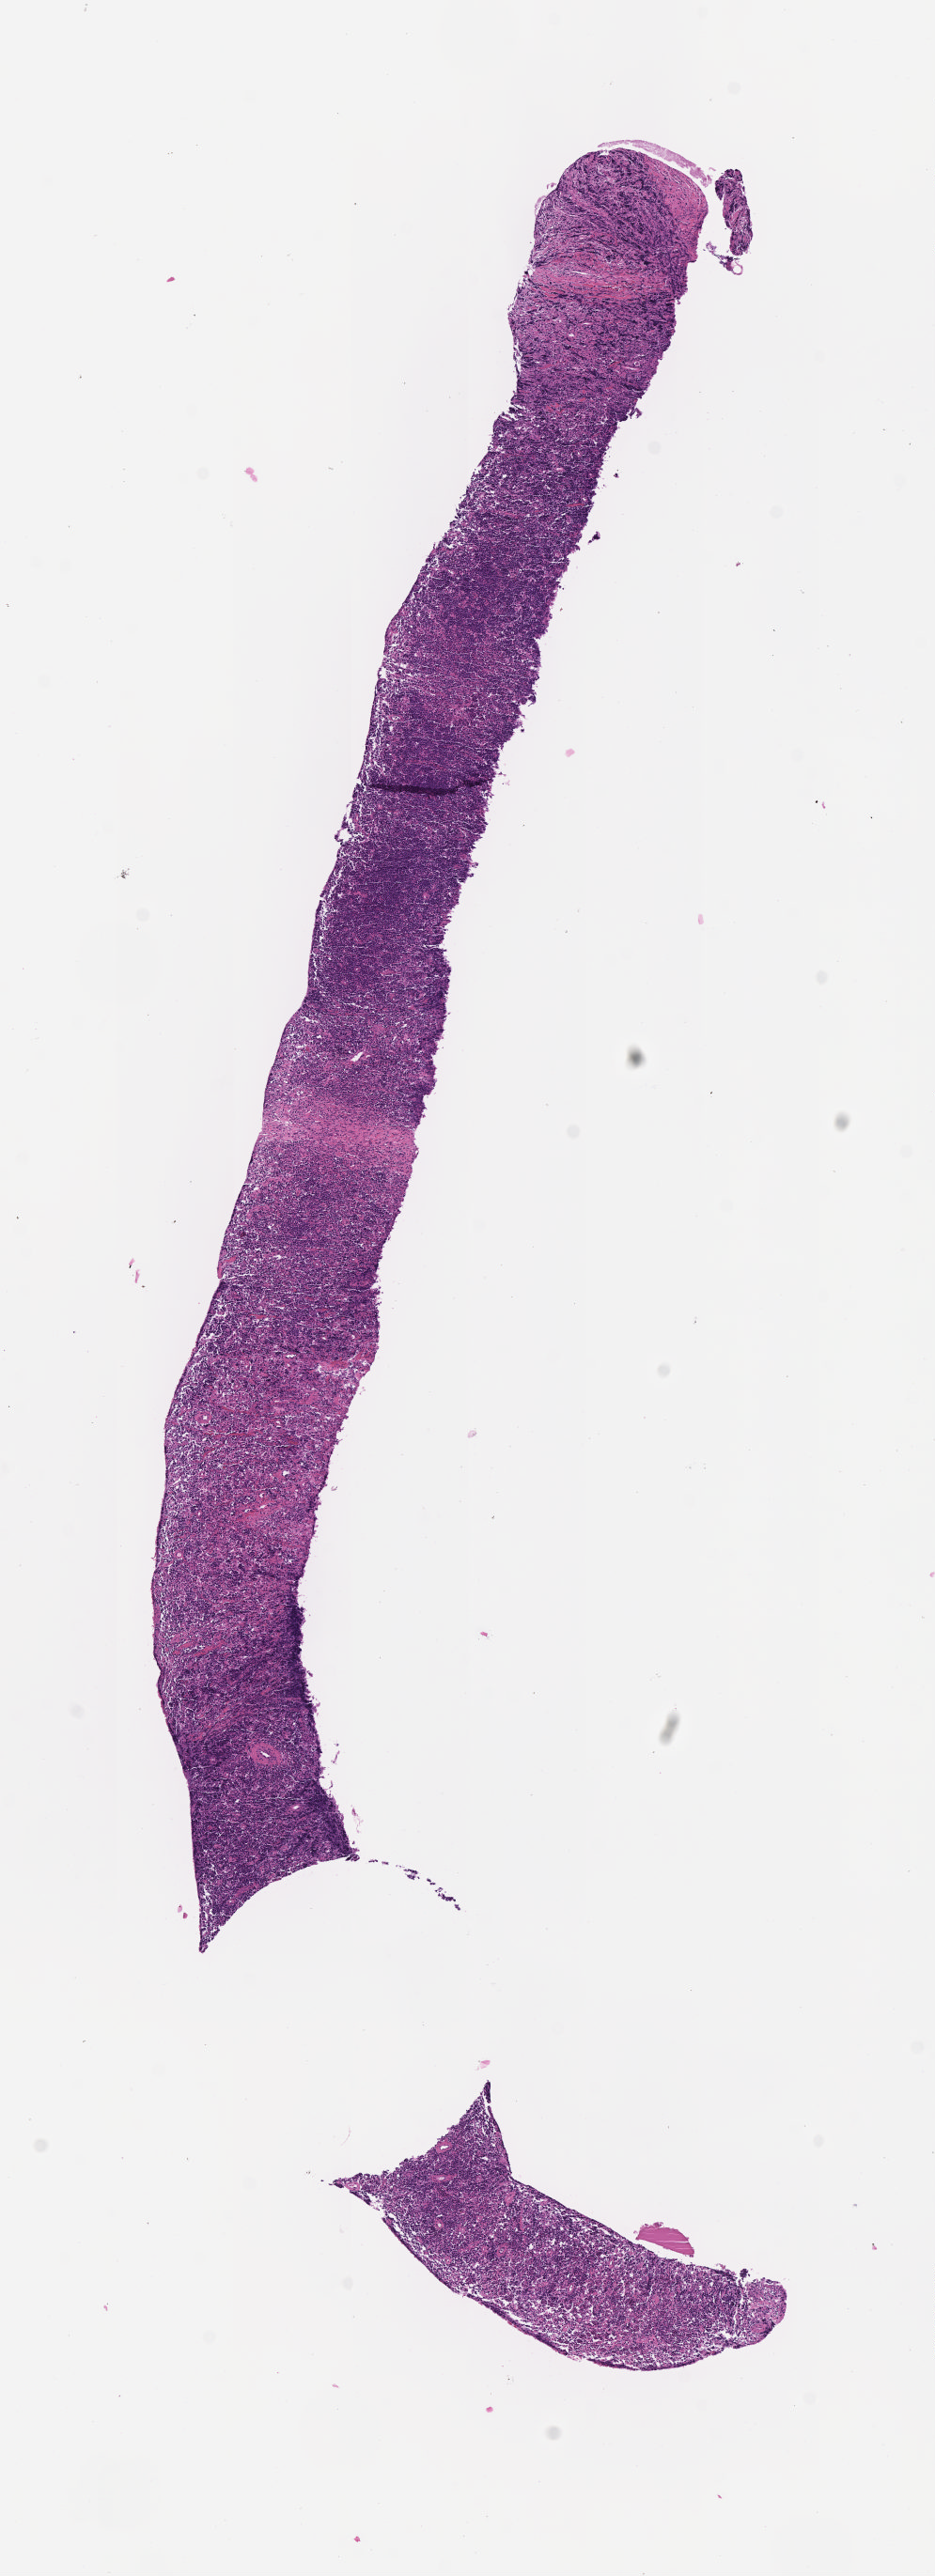
Whole-slide image, H&E stain, shown as a low-resolution overview of the whole scanned area (about 4.0 x 11.1 mm). Specimen: tumor tissue. Site: ovary. Female, age 9 years at initial diagnosis.
Histologic diagnosis: Burkitt lymphoma, NOS.